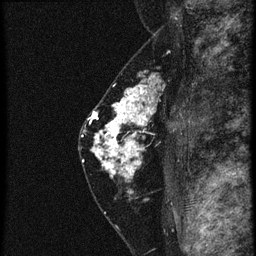
Breast MRI (dynamic contrast-enhanced), one sagittal slice. Position 36 of 60 along the scan axis. 4 images stored at this slice position (order not interpretable as contrast timing). 1.5 T. TE 4.2 ms, TR 20.4 ms. 256 × 256 image matrix, field of view 180 × 180 mm. Female patient, age 46 years. From the clinical record (not read from this slice): setting: breast cancer imaged before/during neoadjuvant chemotherapy; receptor status: triple-negative.
Outlined on this slice (semi-automatic segmentation, software-assisted and operator-edited):
- analysis volume of interest (the breast-tissue region the enhancement analysis was run in; not a lesion): bounding box [x1, y1, x2, y2] px = [88, 82, 179, 185]
- tumour enhancement mask (voxels above the 90 % enhancement threshold inside the analysis volume of interest): [92, 82, 161, 179]